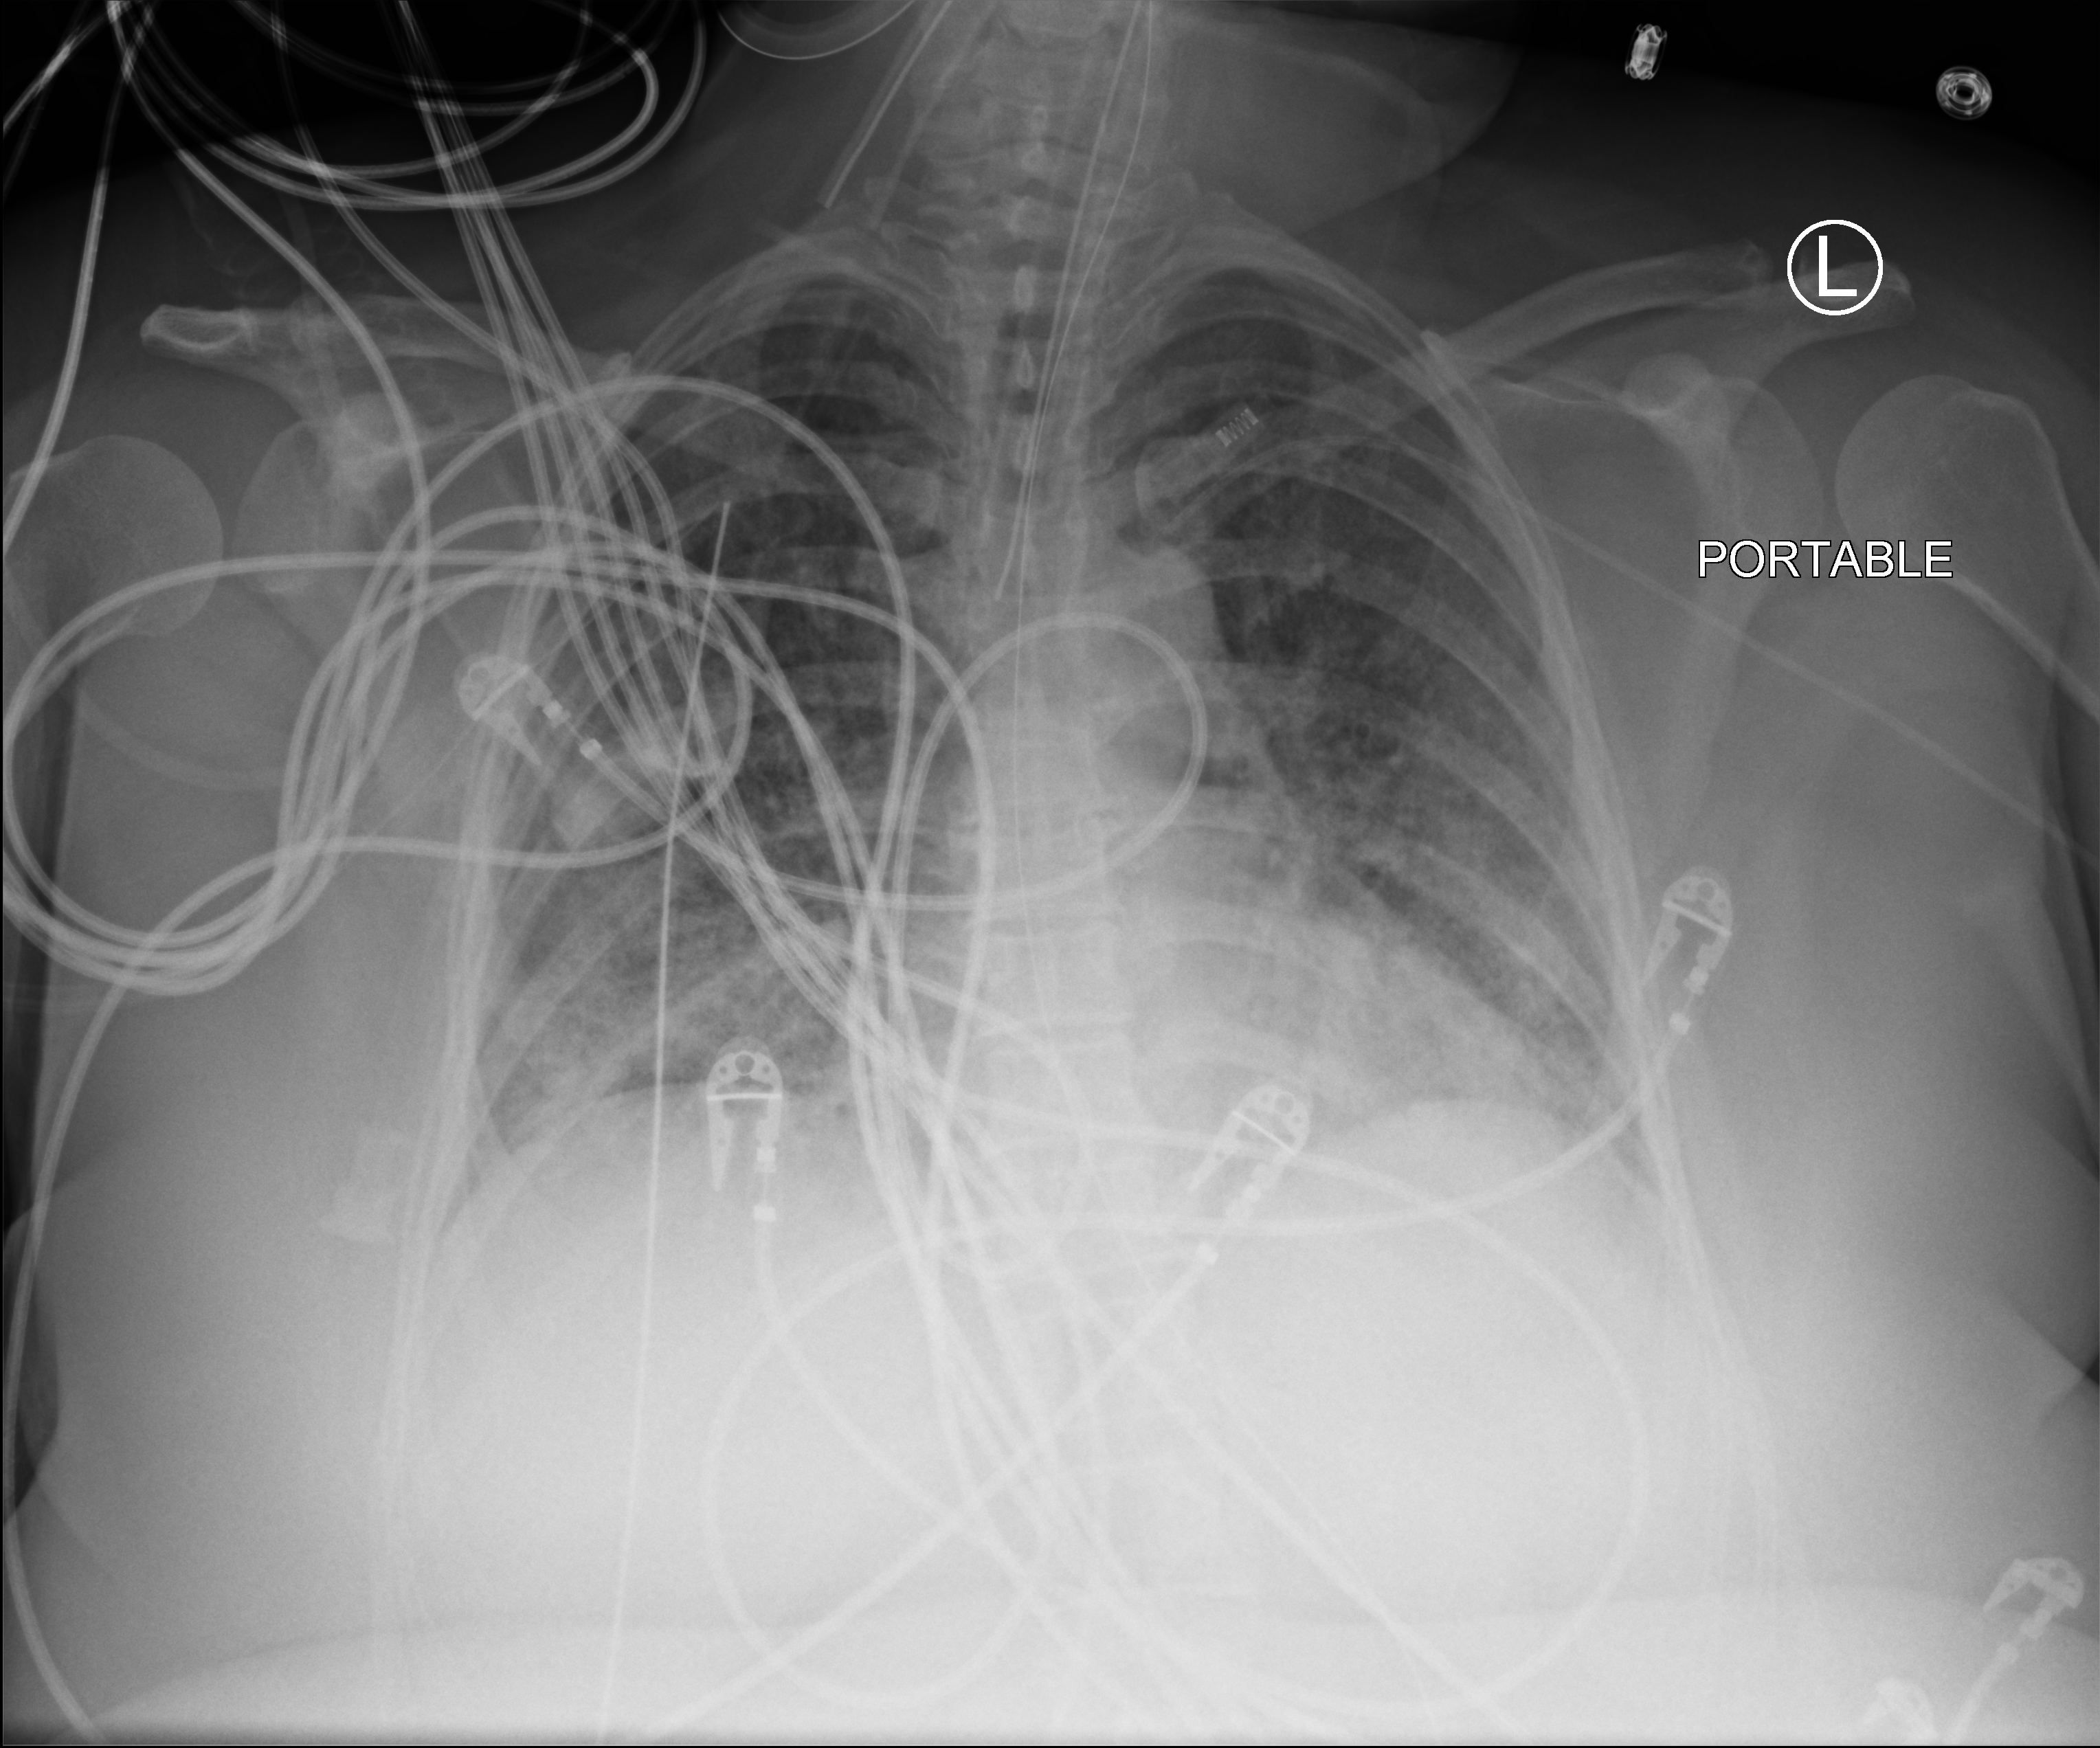
Bedside chest radiograph (computed radiography), anteroposterior (AP) projection. Female patient hospitalised with COVID-19, age 18–59 years.
From the hospital-stay record, not from the radiograph (when in the stay this image was taken is not recorded): admitted to intensive care during this hospital stay: yes; length of hospital stay: 95 days.